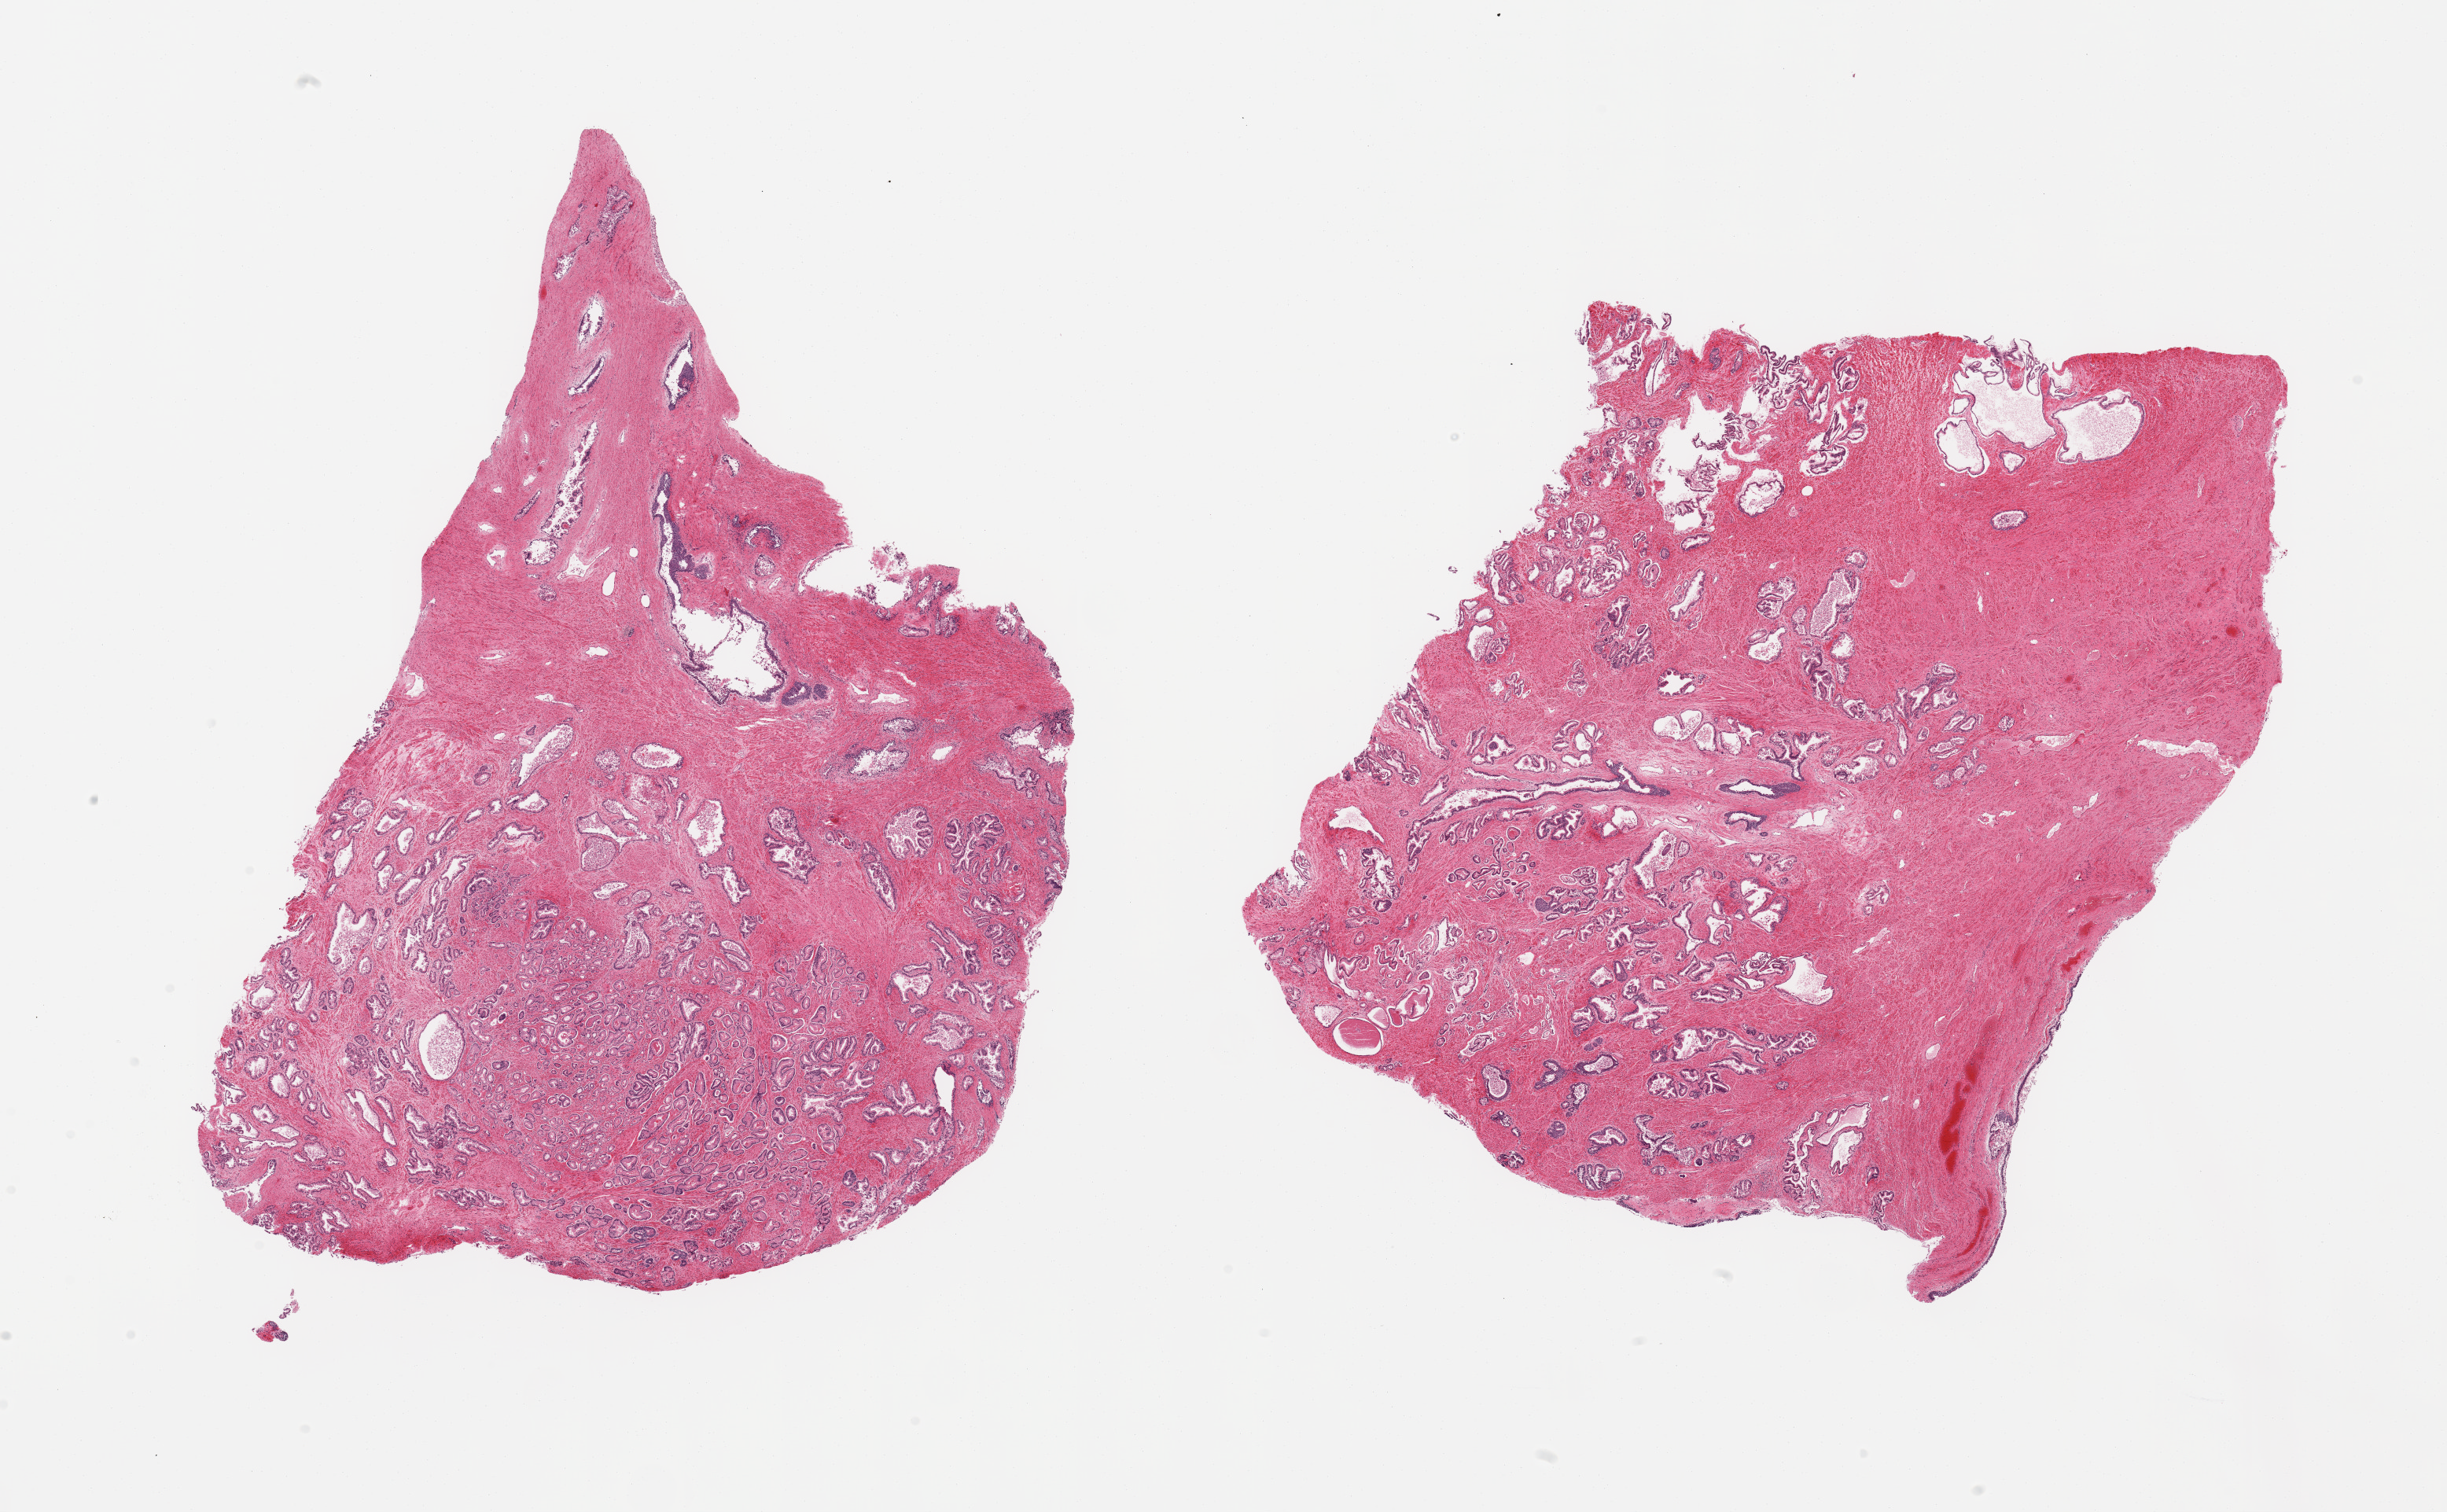
Digitized haematoxylin and eosin-stained section, low-resolution overview of the scanned area, about 24.6 x 15.2 mm (from a 20x scan), PAXgene-fixed, paraffin-embedded tissue, sampled site (target tissue): prostate, donor tissue sample. Male donor.
* review note (as recorded): 2 pieces; mild to moderate autolysis; adenocarcinoma, Gleason grade 3+4